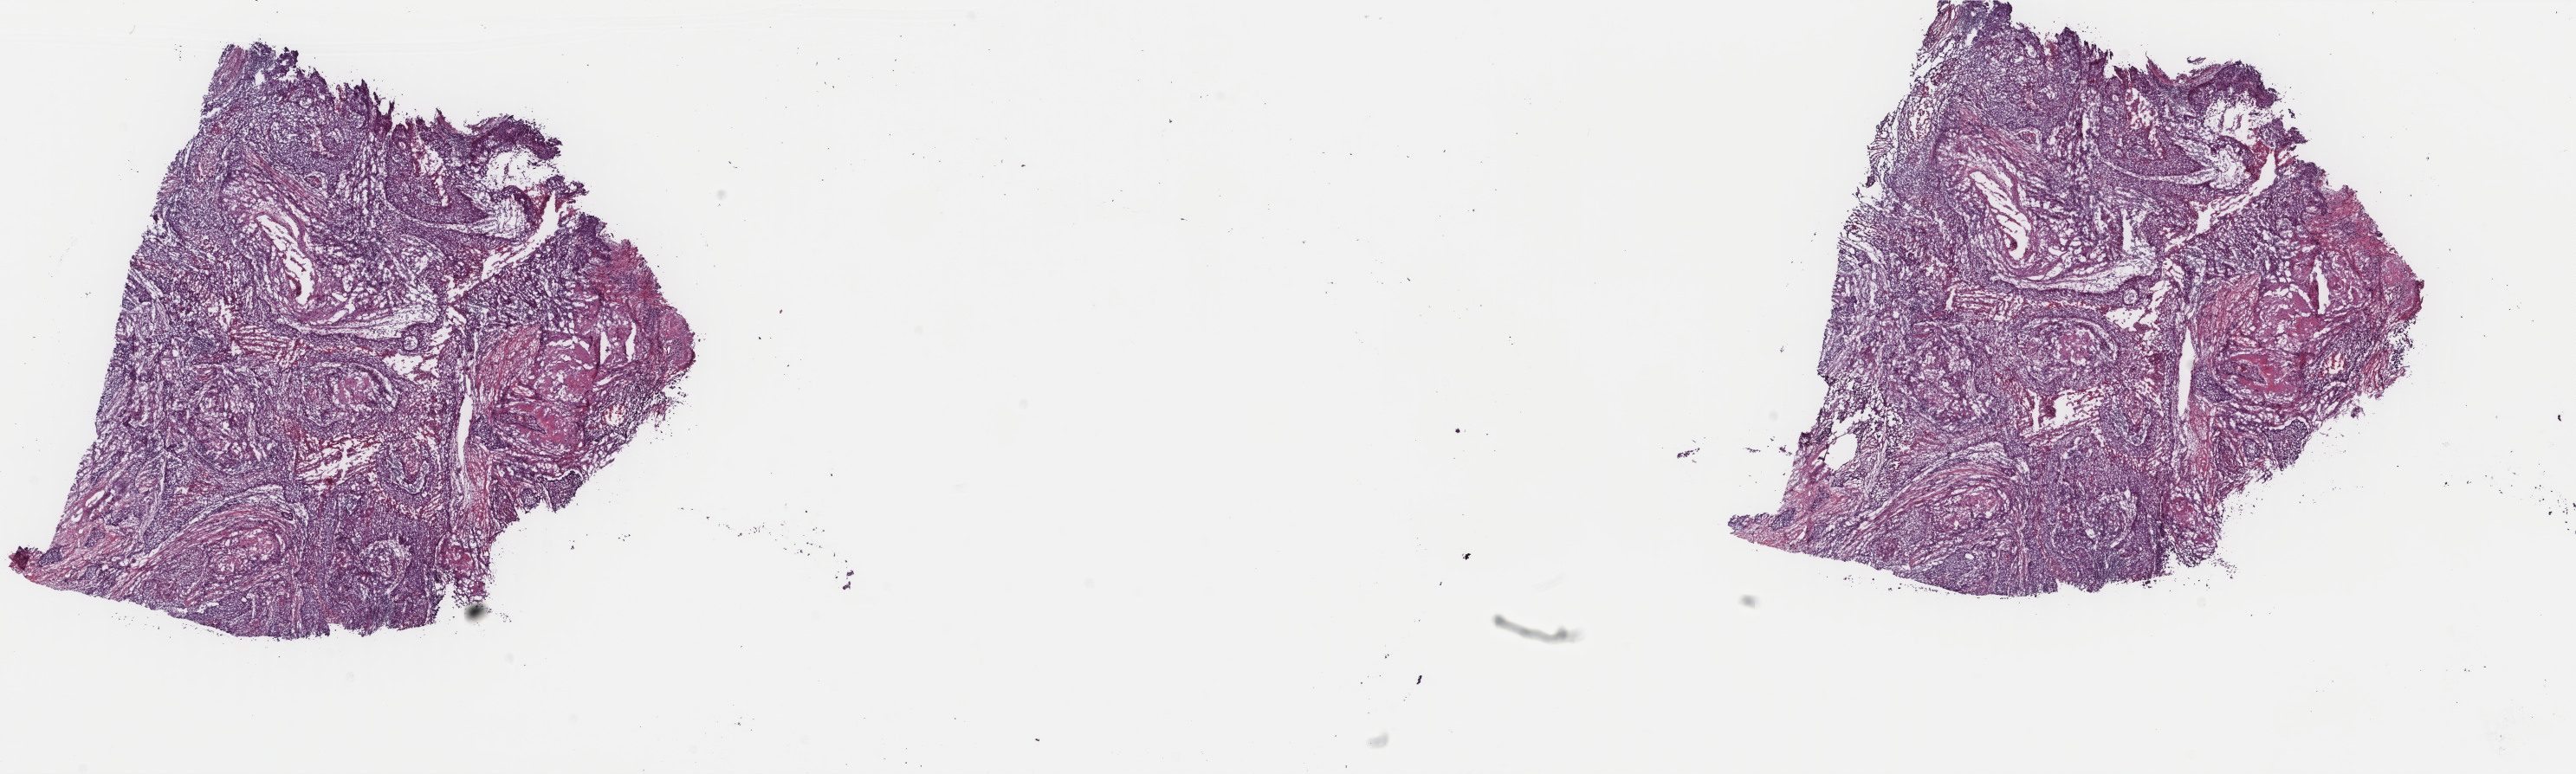
Digitized H&E tissue section (whole slide) — shown as a low-resolution overview of the whole scanned area (about 23.6 x 7.1 mm, from a 40x scan), frozen section from the top of the tissue portion, primary tumour sample from the lung. Male, age 62 years at initial diagnosis. Slide review estimates, as recorded: tumour cells 65%, tumour nuclei 95%, normal cells 0%, stromal cells 20%, necrosis 15%. Infiltration values recorded for this section: lymphocyte infiltration 4%, monocyte infiltration 4%, neutrophil infiltration 8%.
- AJCC pathologic stage: IIB
- TNM: T2b N1 M0
- diagnosis: Squamous cell carcinoma, NOS (lower lobe, lung)